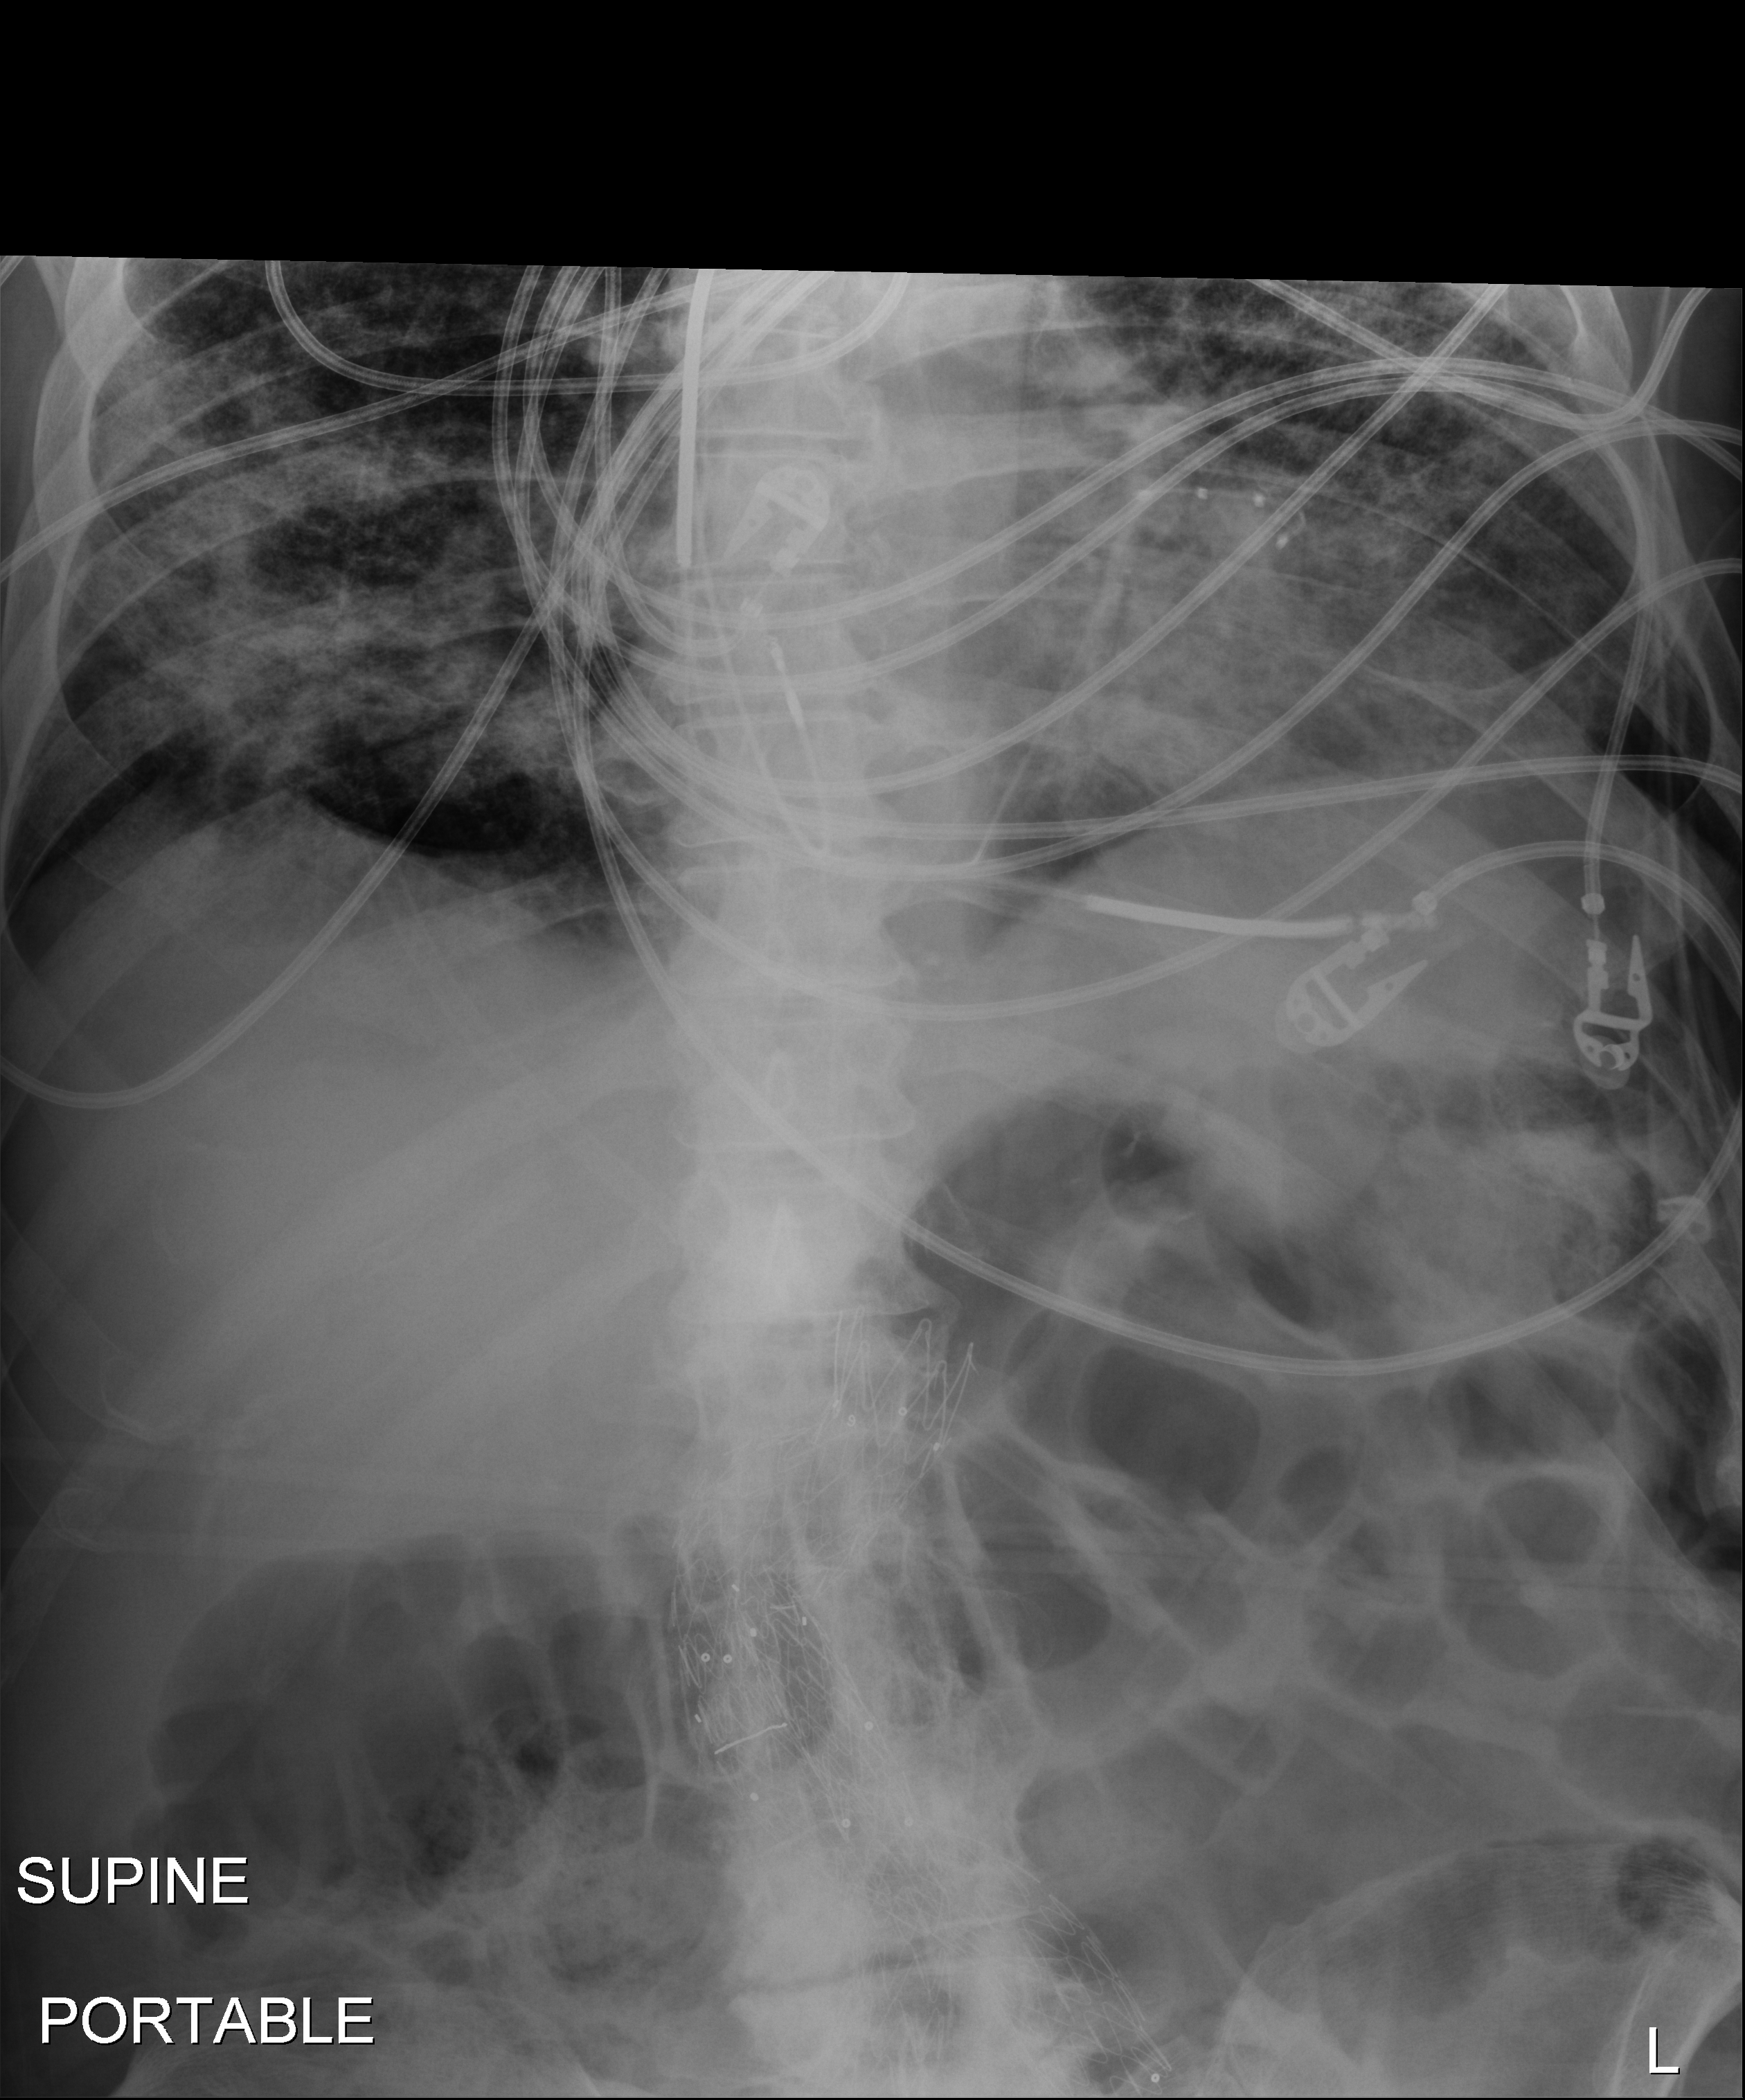
Abdomen X-ray; anteroposterior (AP) projection. Male patient hospitalised with COVID-19, age 60–74 years.
Hospital-stay facts (about this admission, not read from this image; timing relative to this image not recorded):
- length of hospital stay: 36 days
- admitted to intensive care during this hospital stay: yes